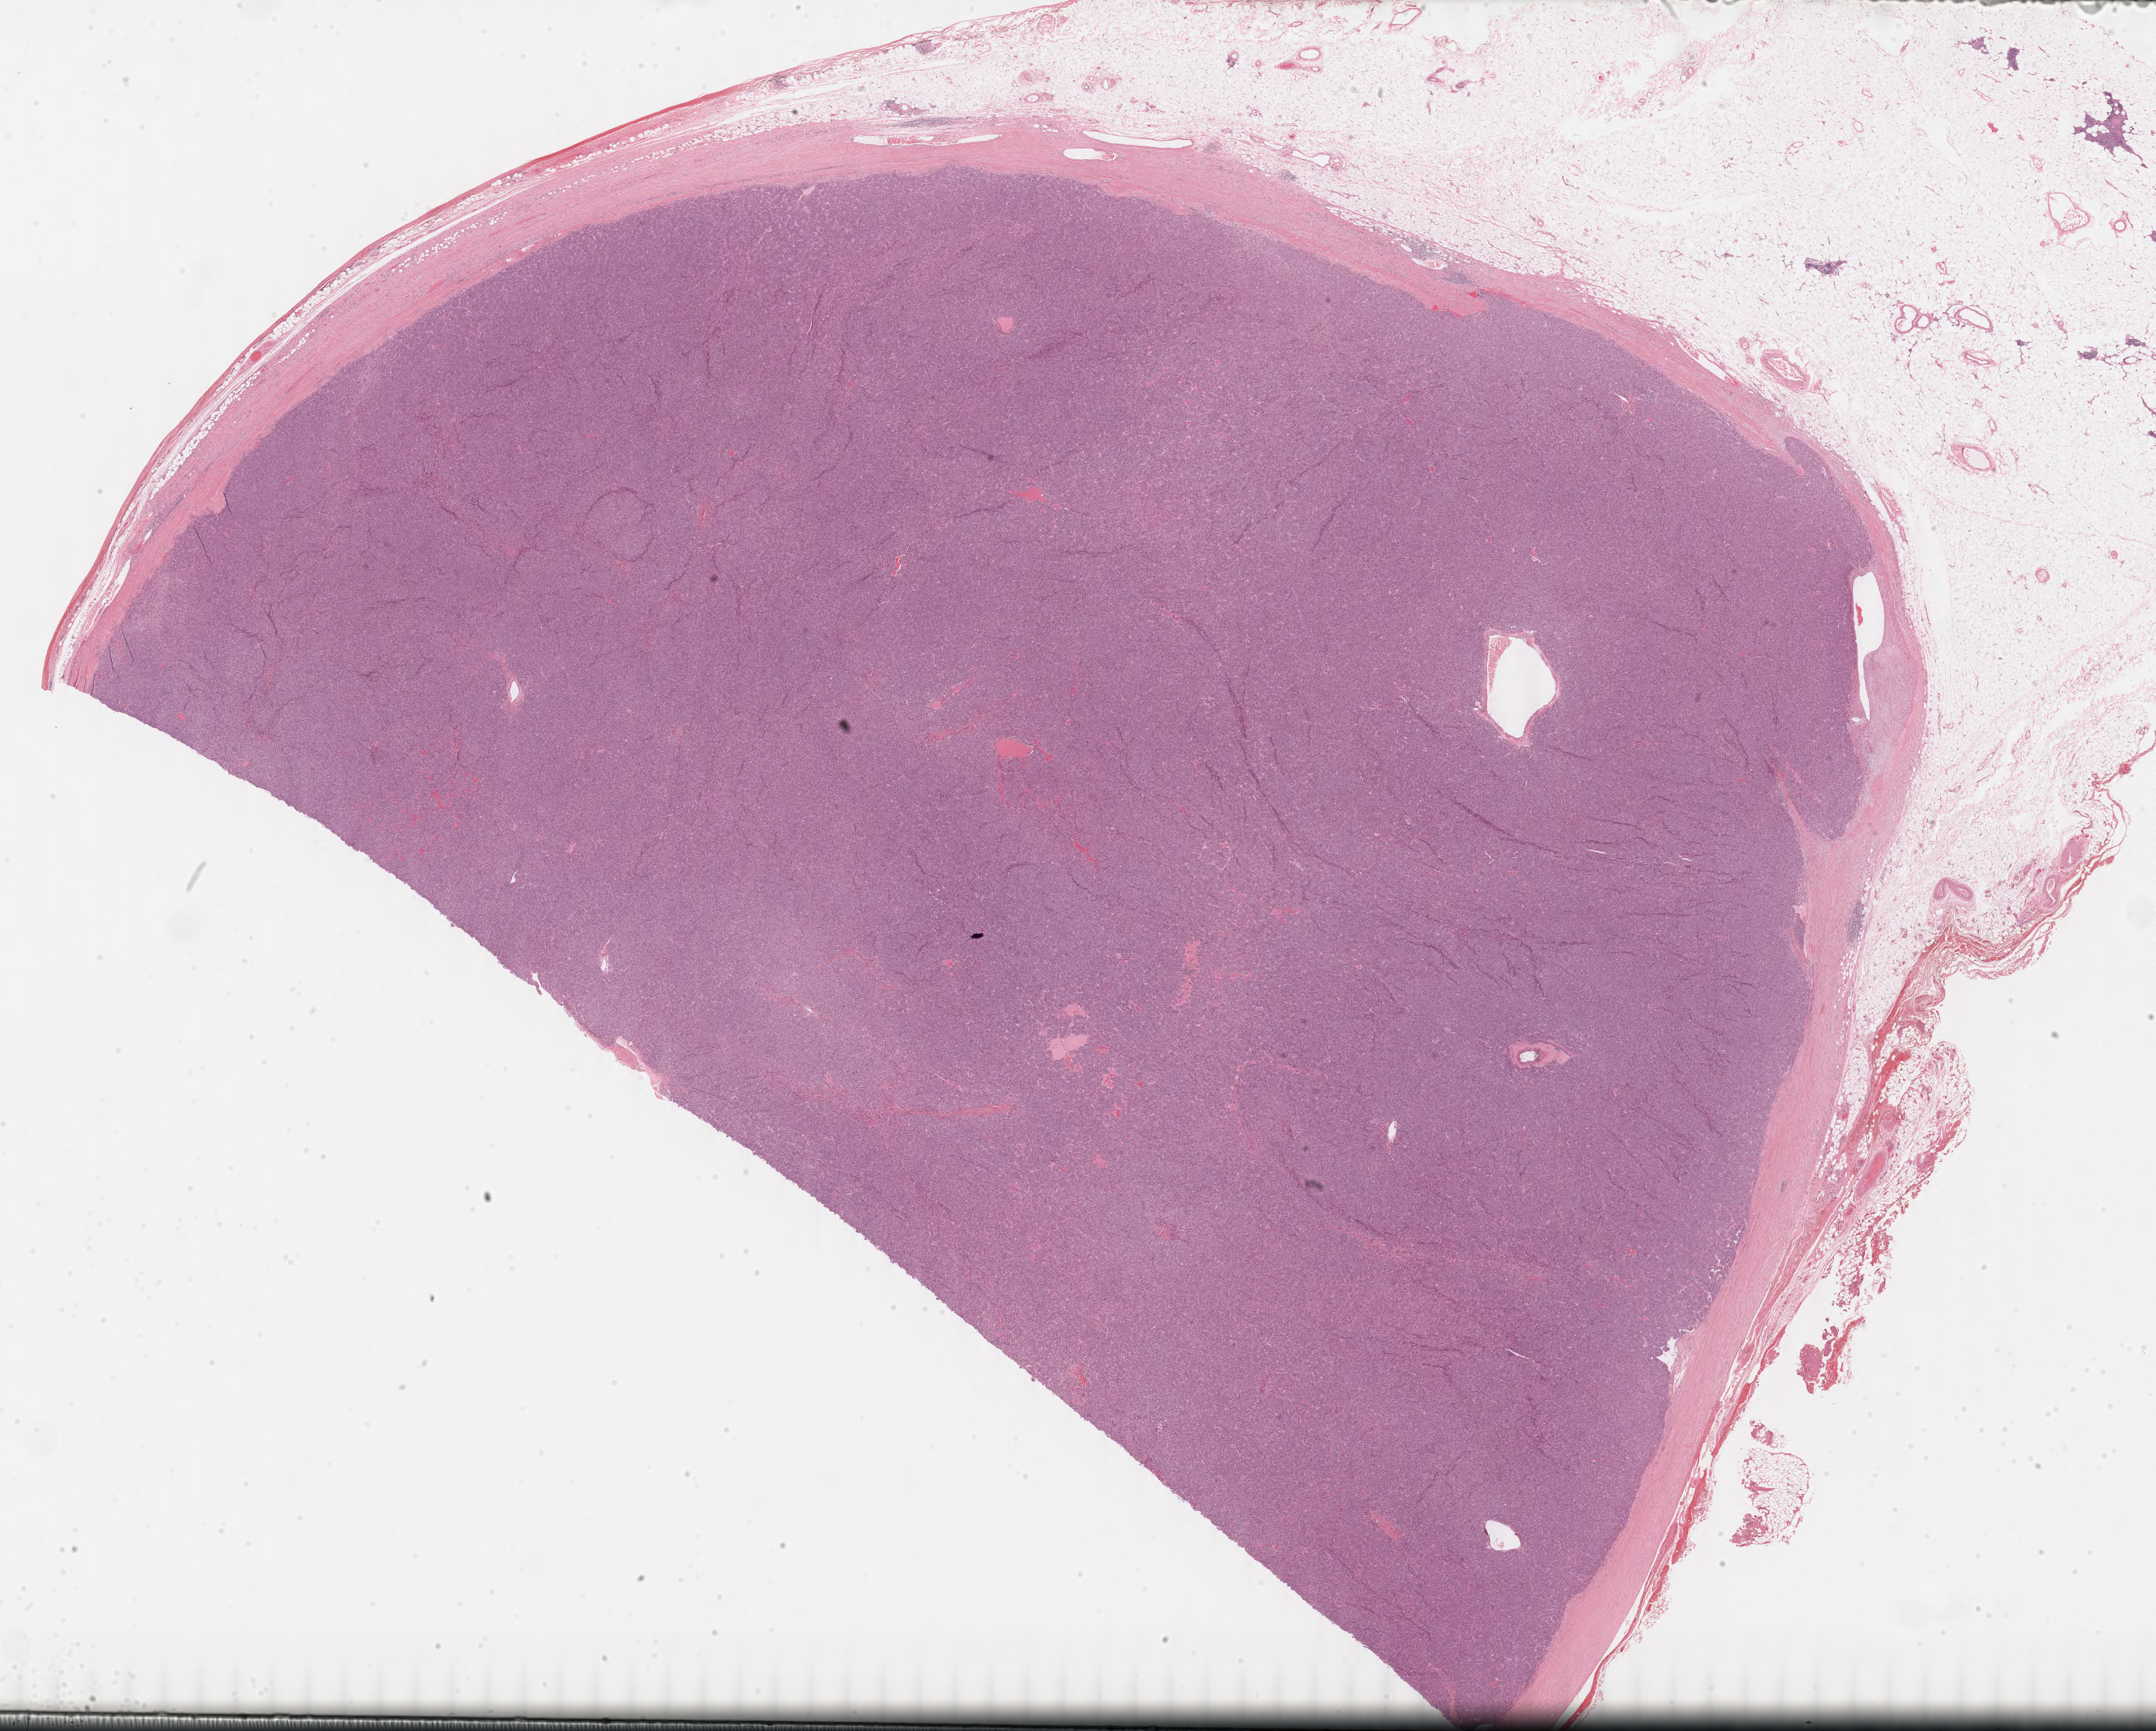
H&E whole-slide image — shown as a low-resolution overview of the whole scanned area (about 29.5 x 23.7 mm); FFPE section; primary tumour sample from the thymus. Male, age 50 years at initial diagnosis.
- pathologic diagnosis: Thymoma, type A, malignant